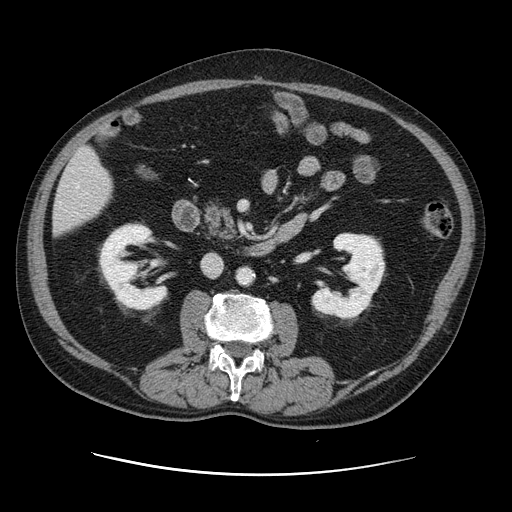
Contrast-enhanced abdominal CT, one axial slice; slice 39 of 141 in the series (ordered by position); intravenous contrast given; soft-tissue window (W 400 / L 40 HU); 2.5 mm slice thickness; 512 × 512 image matrix. Male patient, age 72 years. From the clinical record (not read from this slice): diagnosis: colorectal cancer liver metastases, imaged before liver resection; multiple liver metastases: yes; largest metastasis: 5.4 cm; chemotherapy before resection: yes.
Structures marked on this image (manually delineated by an expert):
- hepatic veins: box from (x=76, y=185) to (x=79, y=188) px
- liver: (x=54, y=148)–(x=112, y=235)
- planned liver remnant (the part of the liver to remain after resection): (x=54, y=149)–(x=112, y=235)